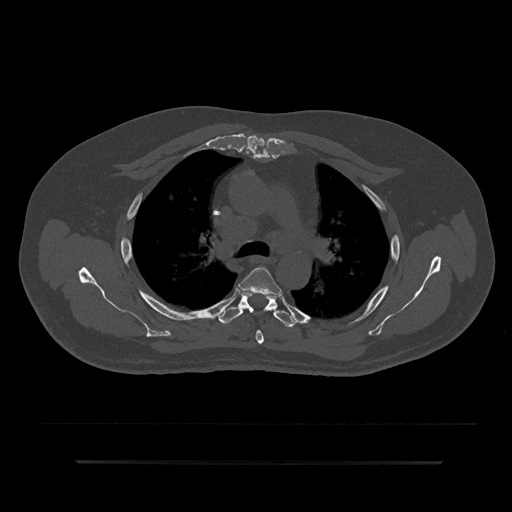
CT including the spine, one axial slice; slice 595 of 797 in the series (ordered by position); reconstruction kernel Br40s/3; 120 kVp; bone window (W 1800 / L 400 HU); 0.5 mm slice thickness; 512 × 512 image matrix. Male patient, age 59 years. From the clinical record (not read from this slice): primary cancer: bile ducts; vertebrae with lytic lesions (as recorded): T10.
Annotated regions visible in this slice (semi-automatic segmentation, software-assisted and operator-edited):
- T4 vertebra: bounding box (x1, y1, x2, y2) in pixels: (238, 267, 282, 344)
- T5 vertebra: (219, 292, 298, 327)